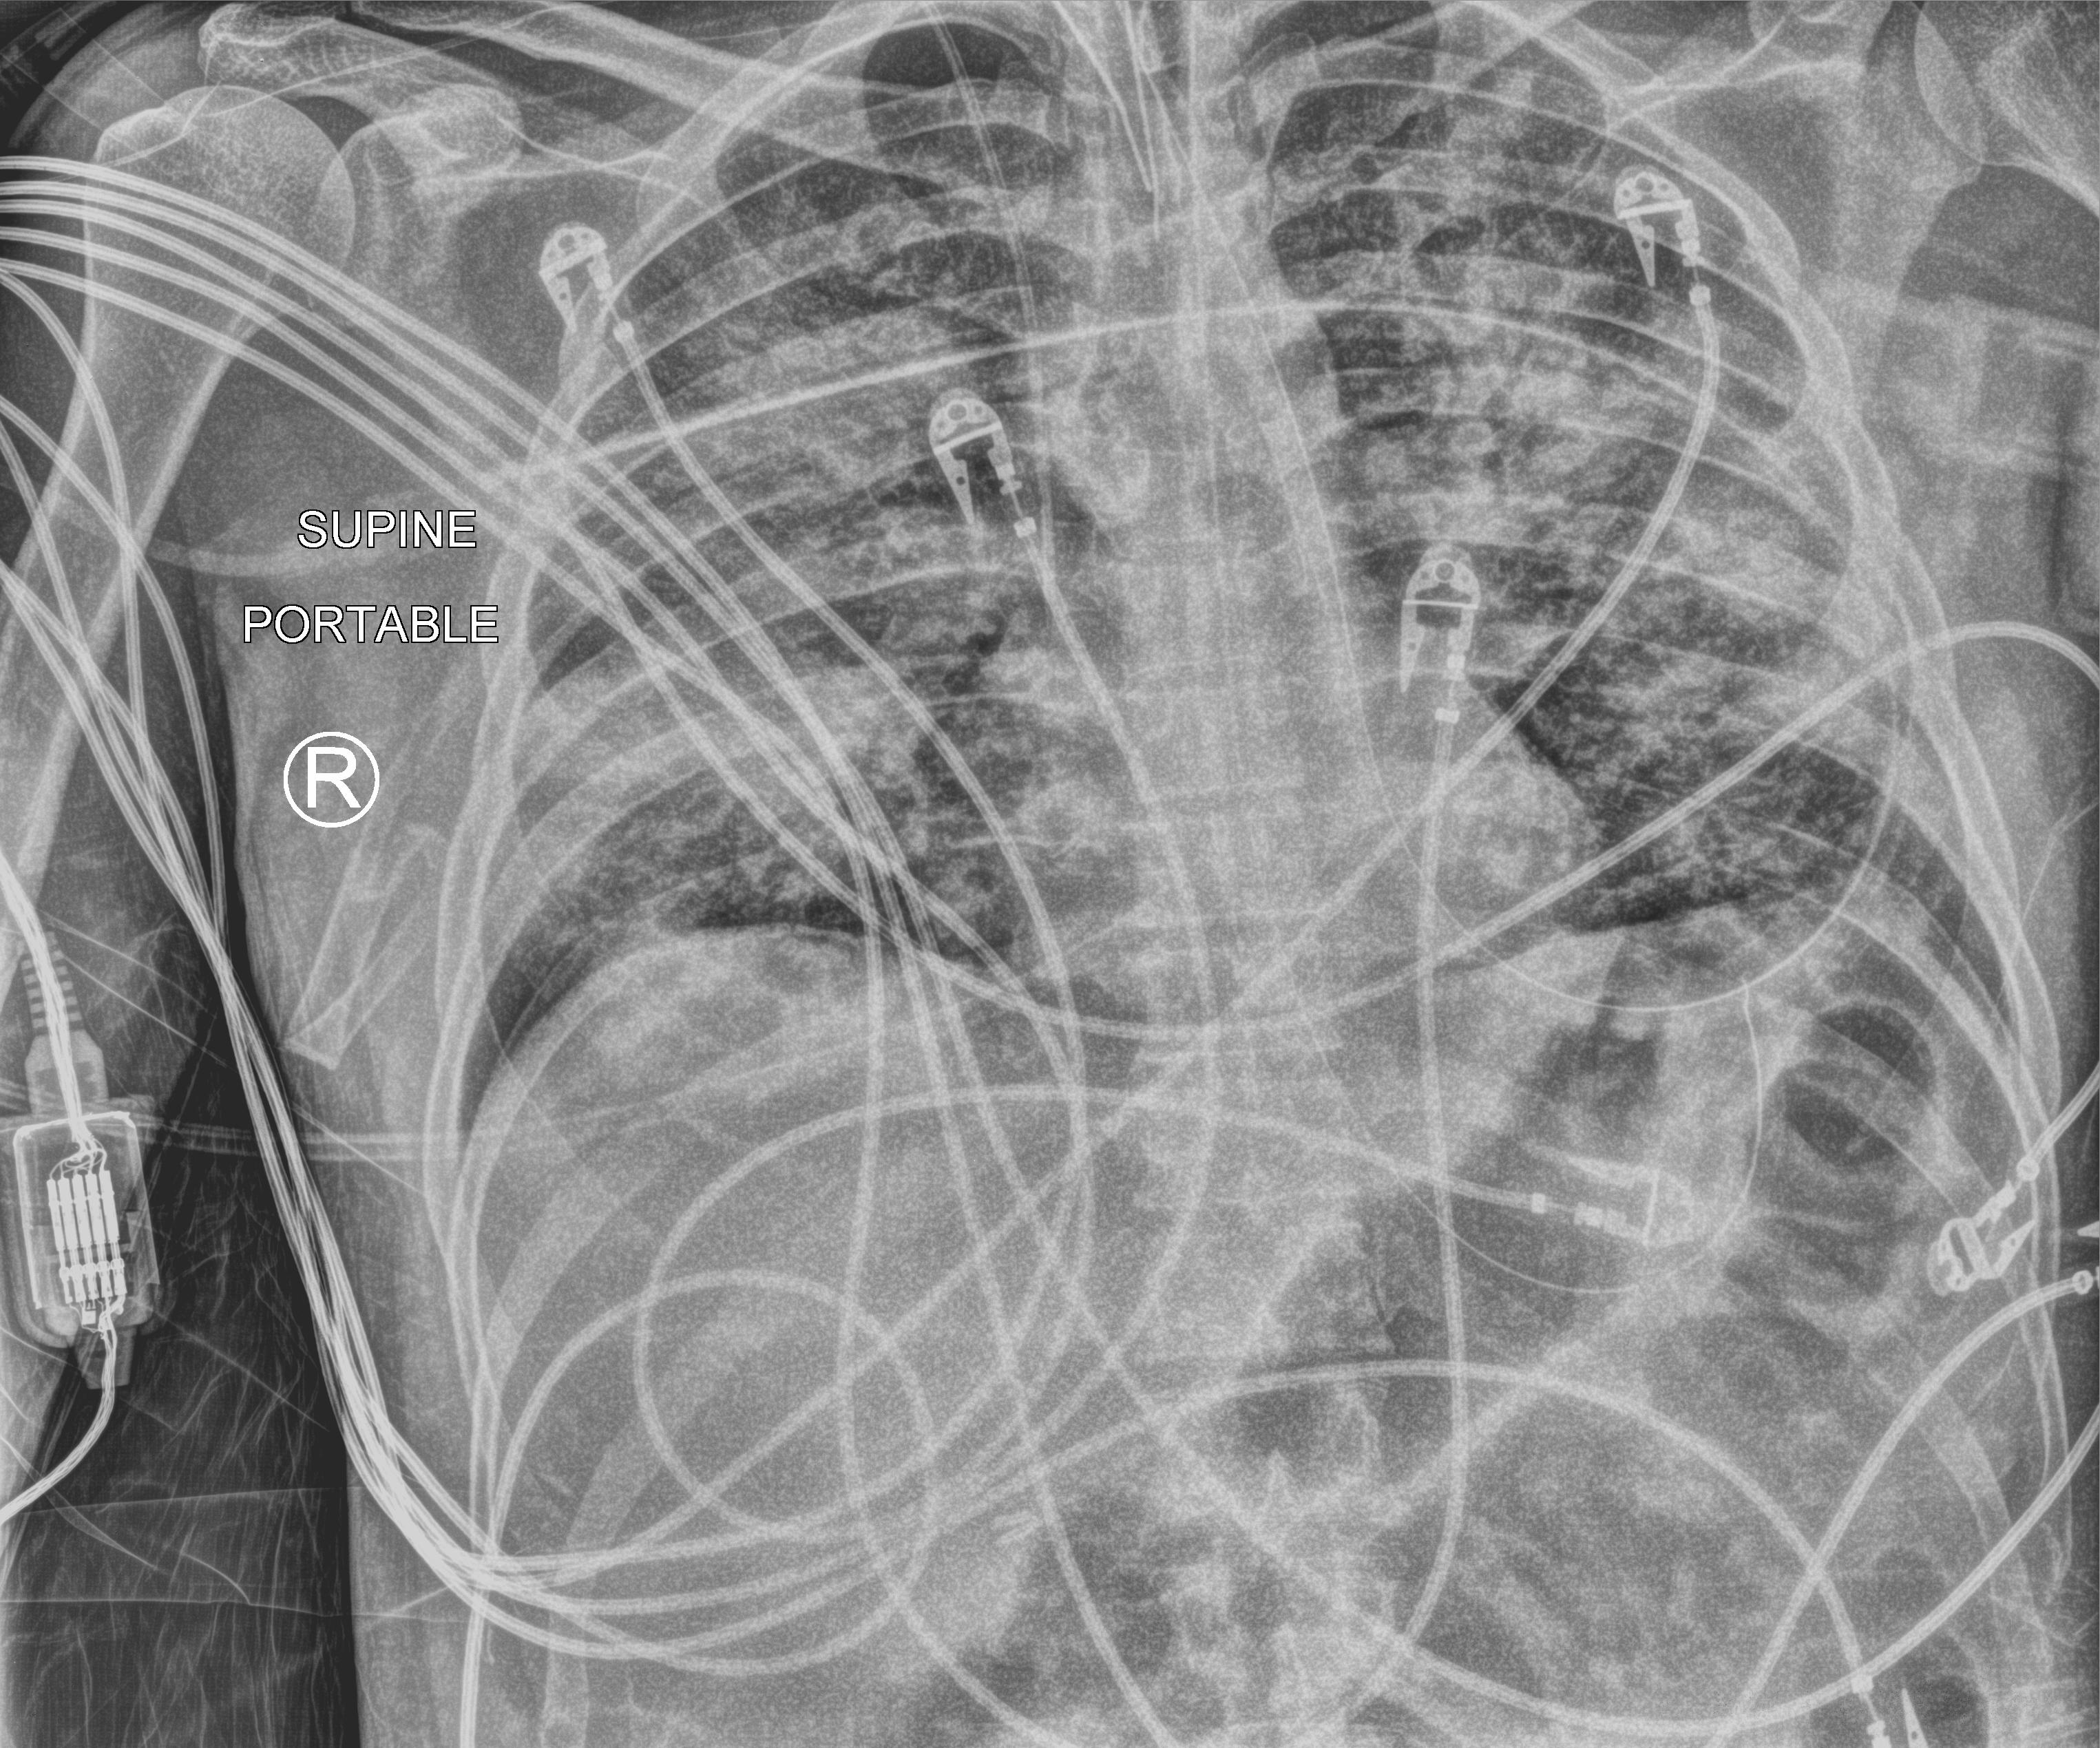
Portable chest radiograph. Male patient hospitalised with COVID-19, age 18–59 years.
Admission-level facts for this patient (not findings on this image; timing relative to this image not recorded): mechanically ventilated during this hospital stay: yes.